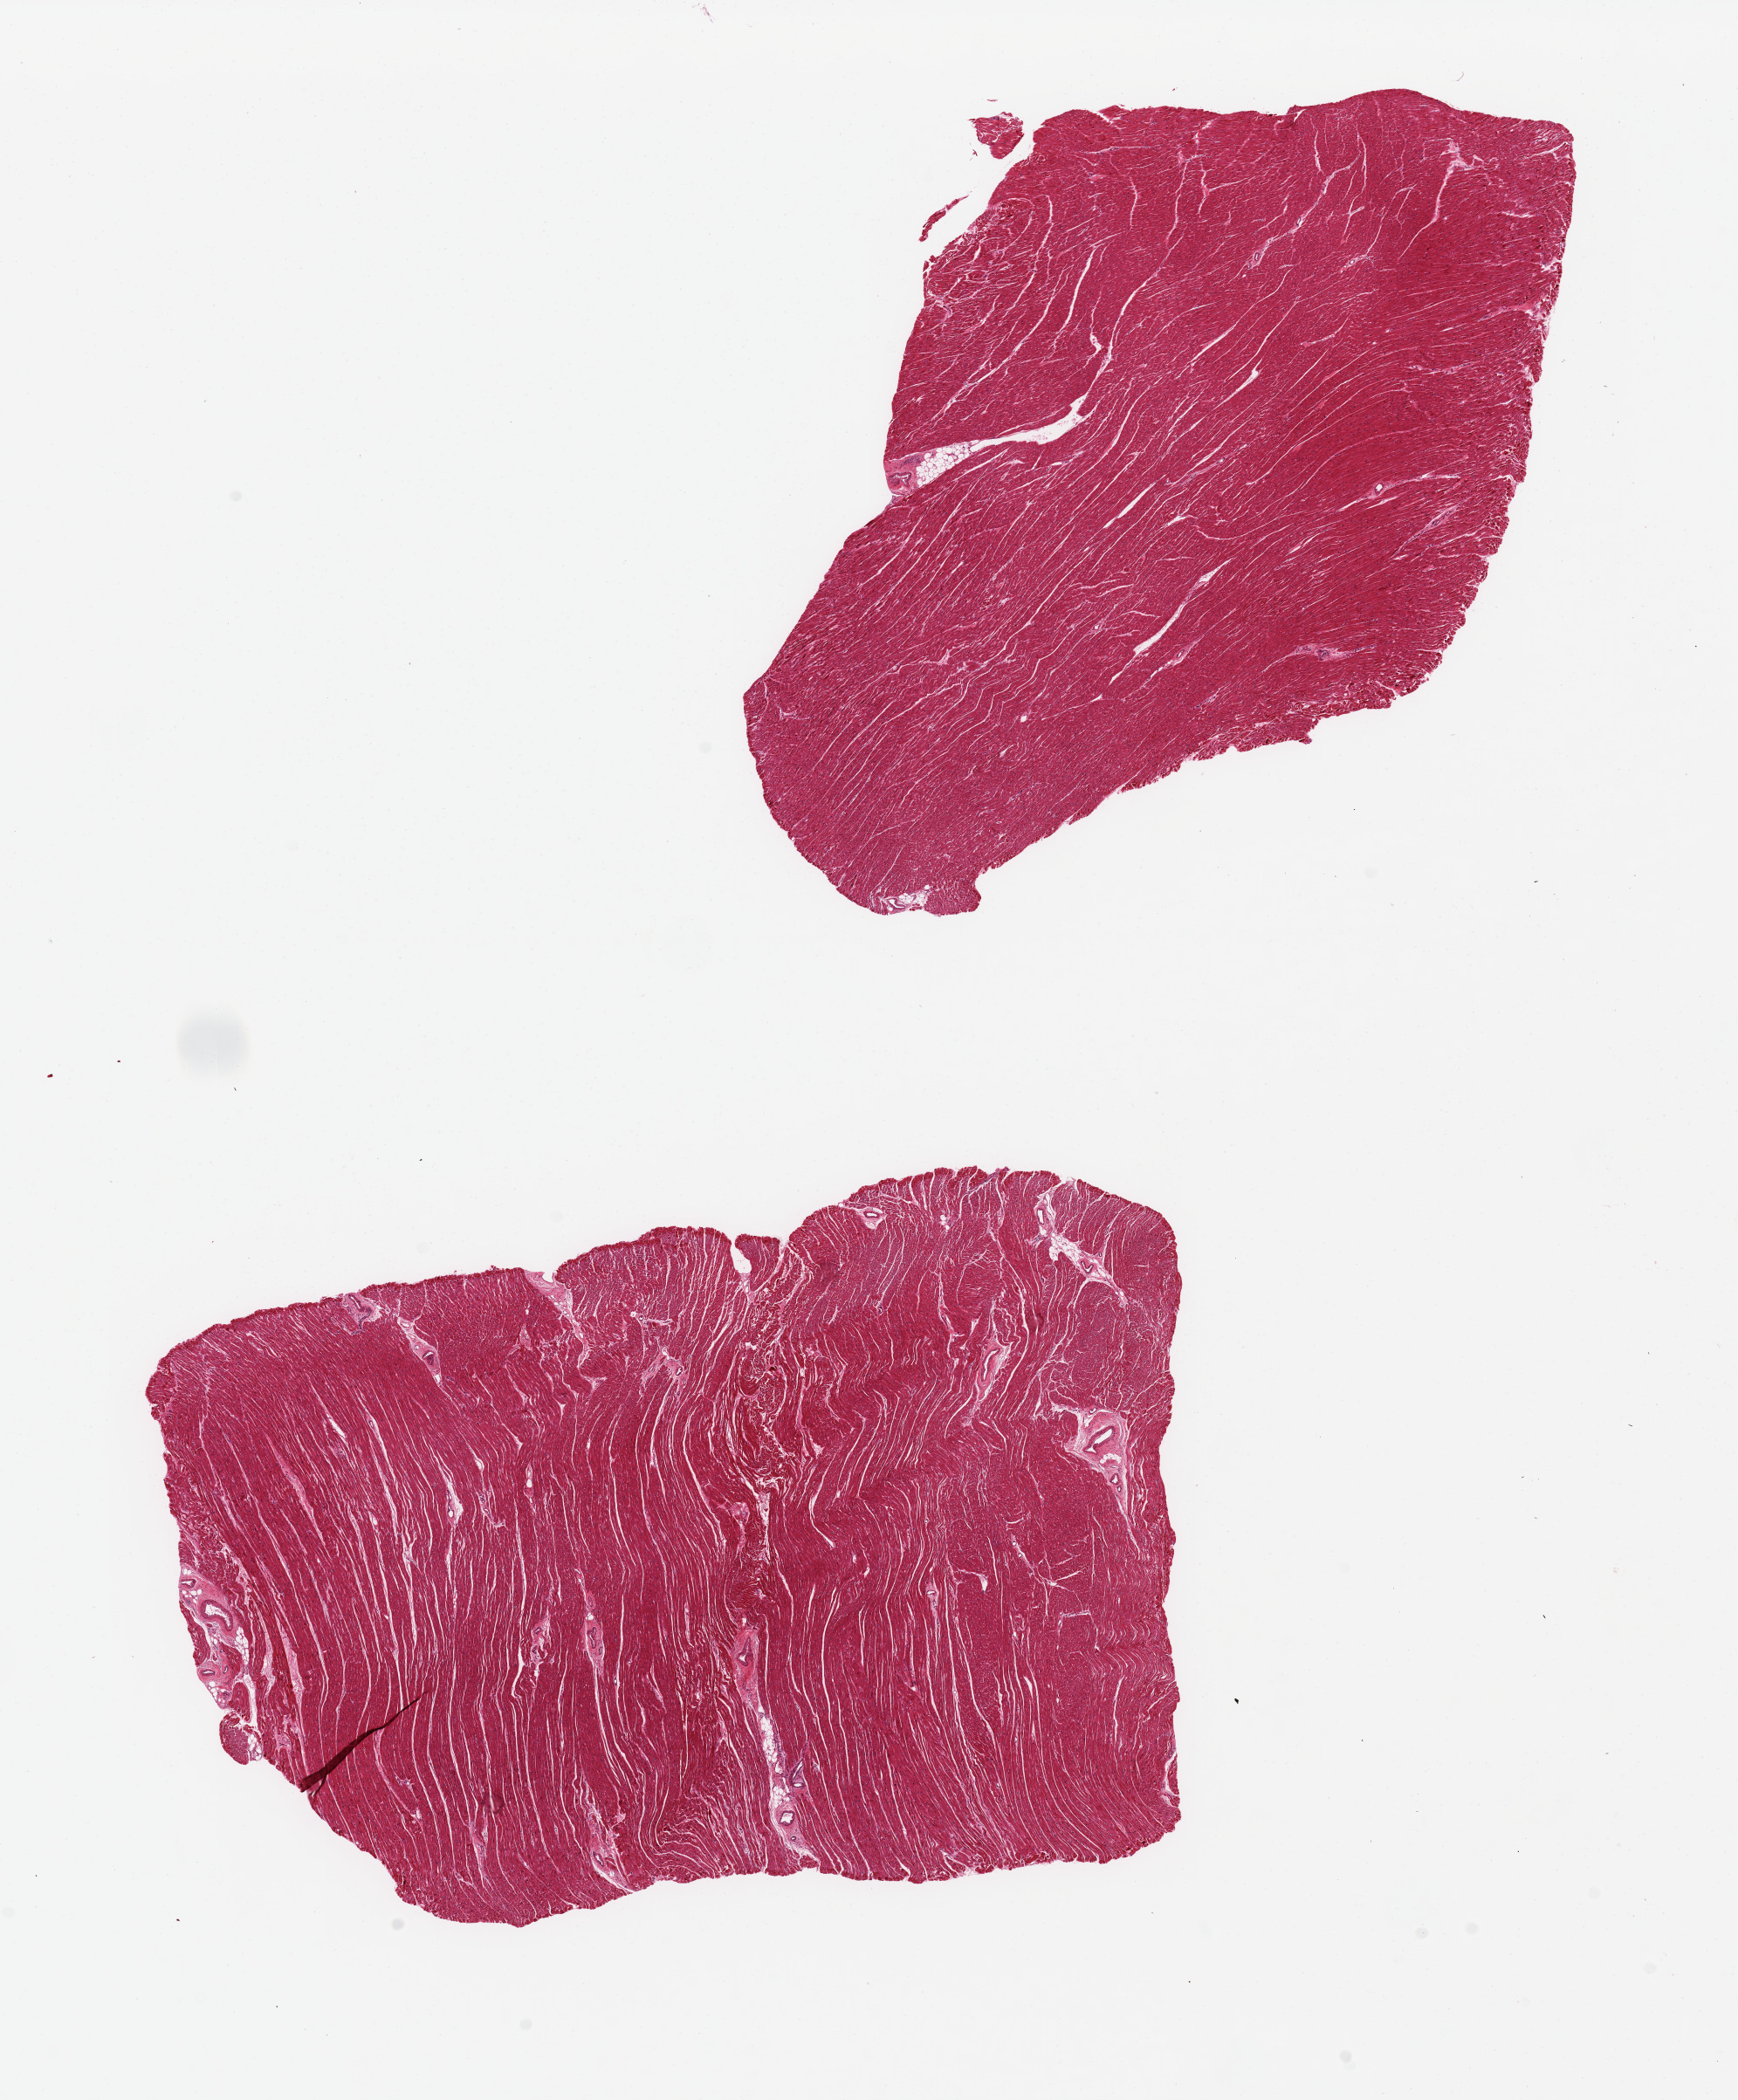
Digitized hematoxylin and eosin (H&E)-stained section — low-resolution overview of the scanned area, about 15.8 x 19.0 mm. PAXgene-fixed, paraffin-embedded tissue. Target tissue: heart. Tissue donor sample.
Review note (as recorded): 2 pieces, 9x6 & 7x6mm; good specimen.